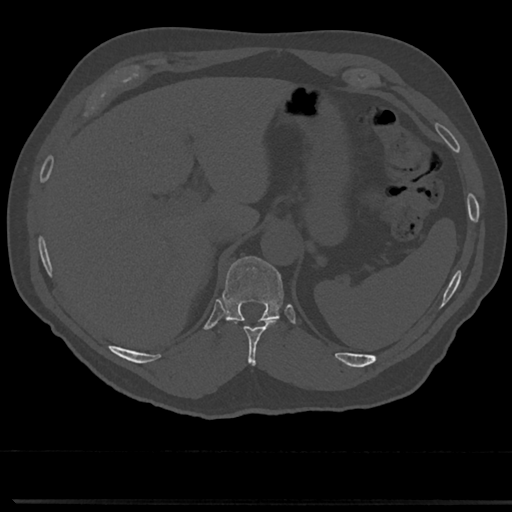
CT including the spine, one axial slice. Position 226 of 817 along the scan axis. Bone window (W 1800 / L 400 HU). 0.5 mm slice thickness. 512 × 512 image matrix. Patient: male, 61 years. Case-level facts recorded for this patient, not image findings: primary cancer: prostate.
Structures marked on this image (semi-automatically segmented with operator editing):
- T10 vertebra: bounding box [x1, y1, x2, y2] px = [230, 318, 279, 365]
- T11 vertebra: [223, 256, 283, 322]